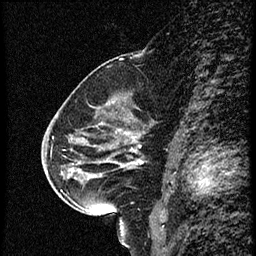
Breast MRI (dynamic contrast-enhanced), one sagittal slice. Position 33 of 56 along the scan axis. Dynamic contrast-enhanced study with each time point stored as its own series, time point 2 of 4 at this slice position (early post-contrast, ordered by acquisition time). 1.5 T. TE 4.2 ms, TR 18.9 ms. 2 mm slice thickness. 256 × 256 image matrix, field of view 200 × 200 mm. Female patient. From the clinical record (not read from this slice): setting: breast cancer imaged before/during neoadjuvant chemotherapy; receptor status: HER2-positive.
Annotated regions visible in this slice (semi-automatic segmentation, software-assisted and operator-edited):
- analysis volume of interest (the breast-tissue region the enhancement analysis was run in; not a lesion): box from (x=63, y=80) to (x=161, y=215) px
- tumour enhancement mask (voxels above the 100 % enhancement threshold inside the analysis volume of interest): (x=90, y=160)–(x=141, y=177)